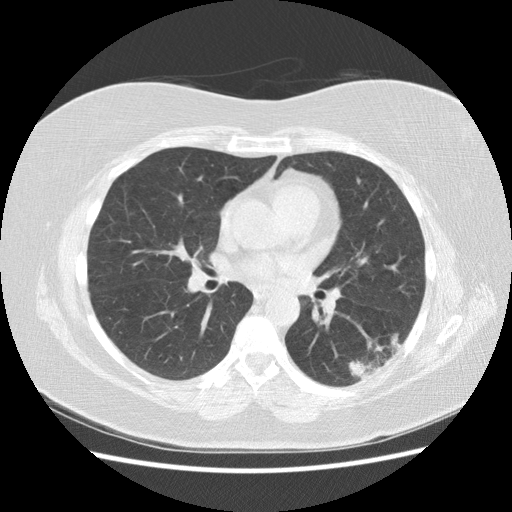
Axial slice from a low-dose chest CT screening exam; third annual screen; lung window (W 1500 / L -600 HU); 2.5 mm slice thickness; 120 kVp; slice 81 of 151 in the series. Female, age 57 years at enrolment.
- Expert-annotated lung lesion, bounding box [x1, y1, x2, y2] px = [334, 325, 410, 388].
- The exam's reader record, not a measurement of the box and not confirmed to be the same lesion: non-calcified nodule or mass ≥4 mm, left lower lobe, 40 × 20 mm, poorly defined margins, mixed attenuation, pre-existing on the prior screen: yes; interval growth: yes.
- Official screen result: positive, other.
- Participant outcome: lung cancer diagnosed 55 days after this screen — squamous cell carcinoma, NOS, left lower lobe, poorly differentiated (G3), stage IB (AJCC 6th edition), 40 mm at pathology.